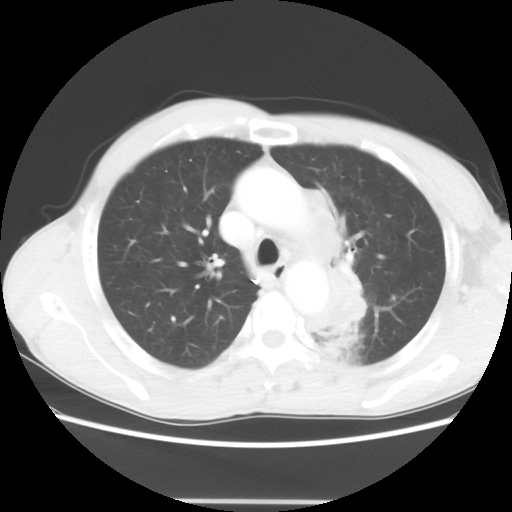
Chest CT, one axial slice. Slice 46 of 62 in the series (ordered by position). Reconstruction kernel STANDARD. Lung window (W 1500 / L -600 HU). 5 mm slice thickness. 512 × 512 image matrix, field of view 360 × 360 mm. Patient: male, 61 years. From the clinical record (not read from this slice): clinical TNM (as recorded): T3 N1 M1.
Outlined on this slice (bounding box drawn by a radiologist):
- lung tumour (recorded histology: adenocarcinoma): bounding box (x1, y1, x2, y2) in pixels: (305, 186, 366, 342)